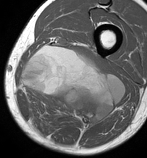
MRI of an extremity soft-tissue mass, one axial slice. Slice 41 of 86 in the series (ordered by position). MR volume resampled by the dataset authors to the PET/CT grid (not the native acquisition matrix). 147 × 158 image matrix. Male patient. From the clinical record (not read from this slice): histological type: undifferentiated pleomorphic liposarcoma; grade: high; site of the primary tumour: left thigh.
Structures marked on this image (expert contour drawn on MRI and transferred to this co-registered scan by the dataset authors):
- gross tumour volume including surrounding oedema: bounding box <21,46,125,128> (left, top, right, bottom; pixels)
- gross tumour volume (mass): <21,46,125,128>